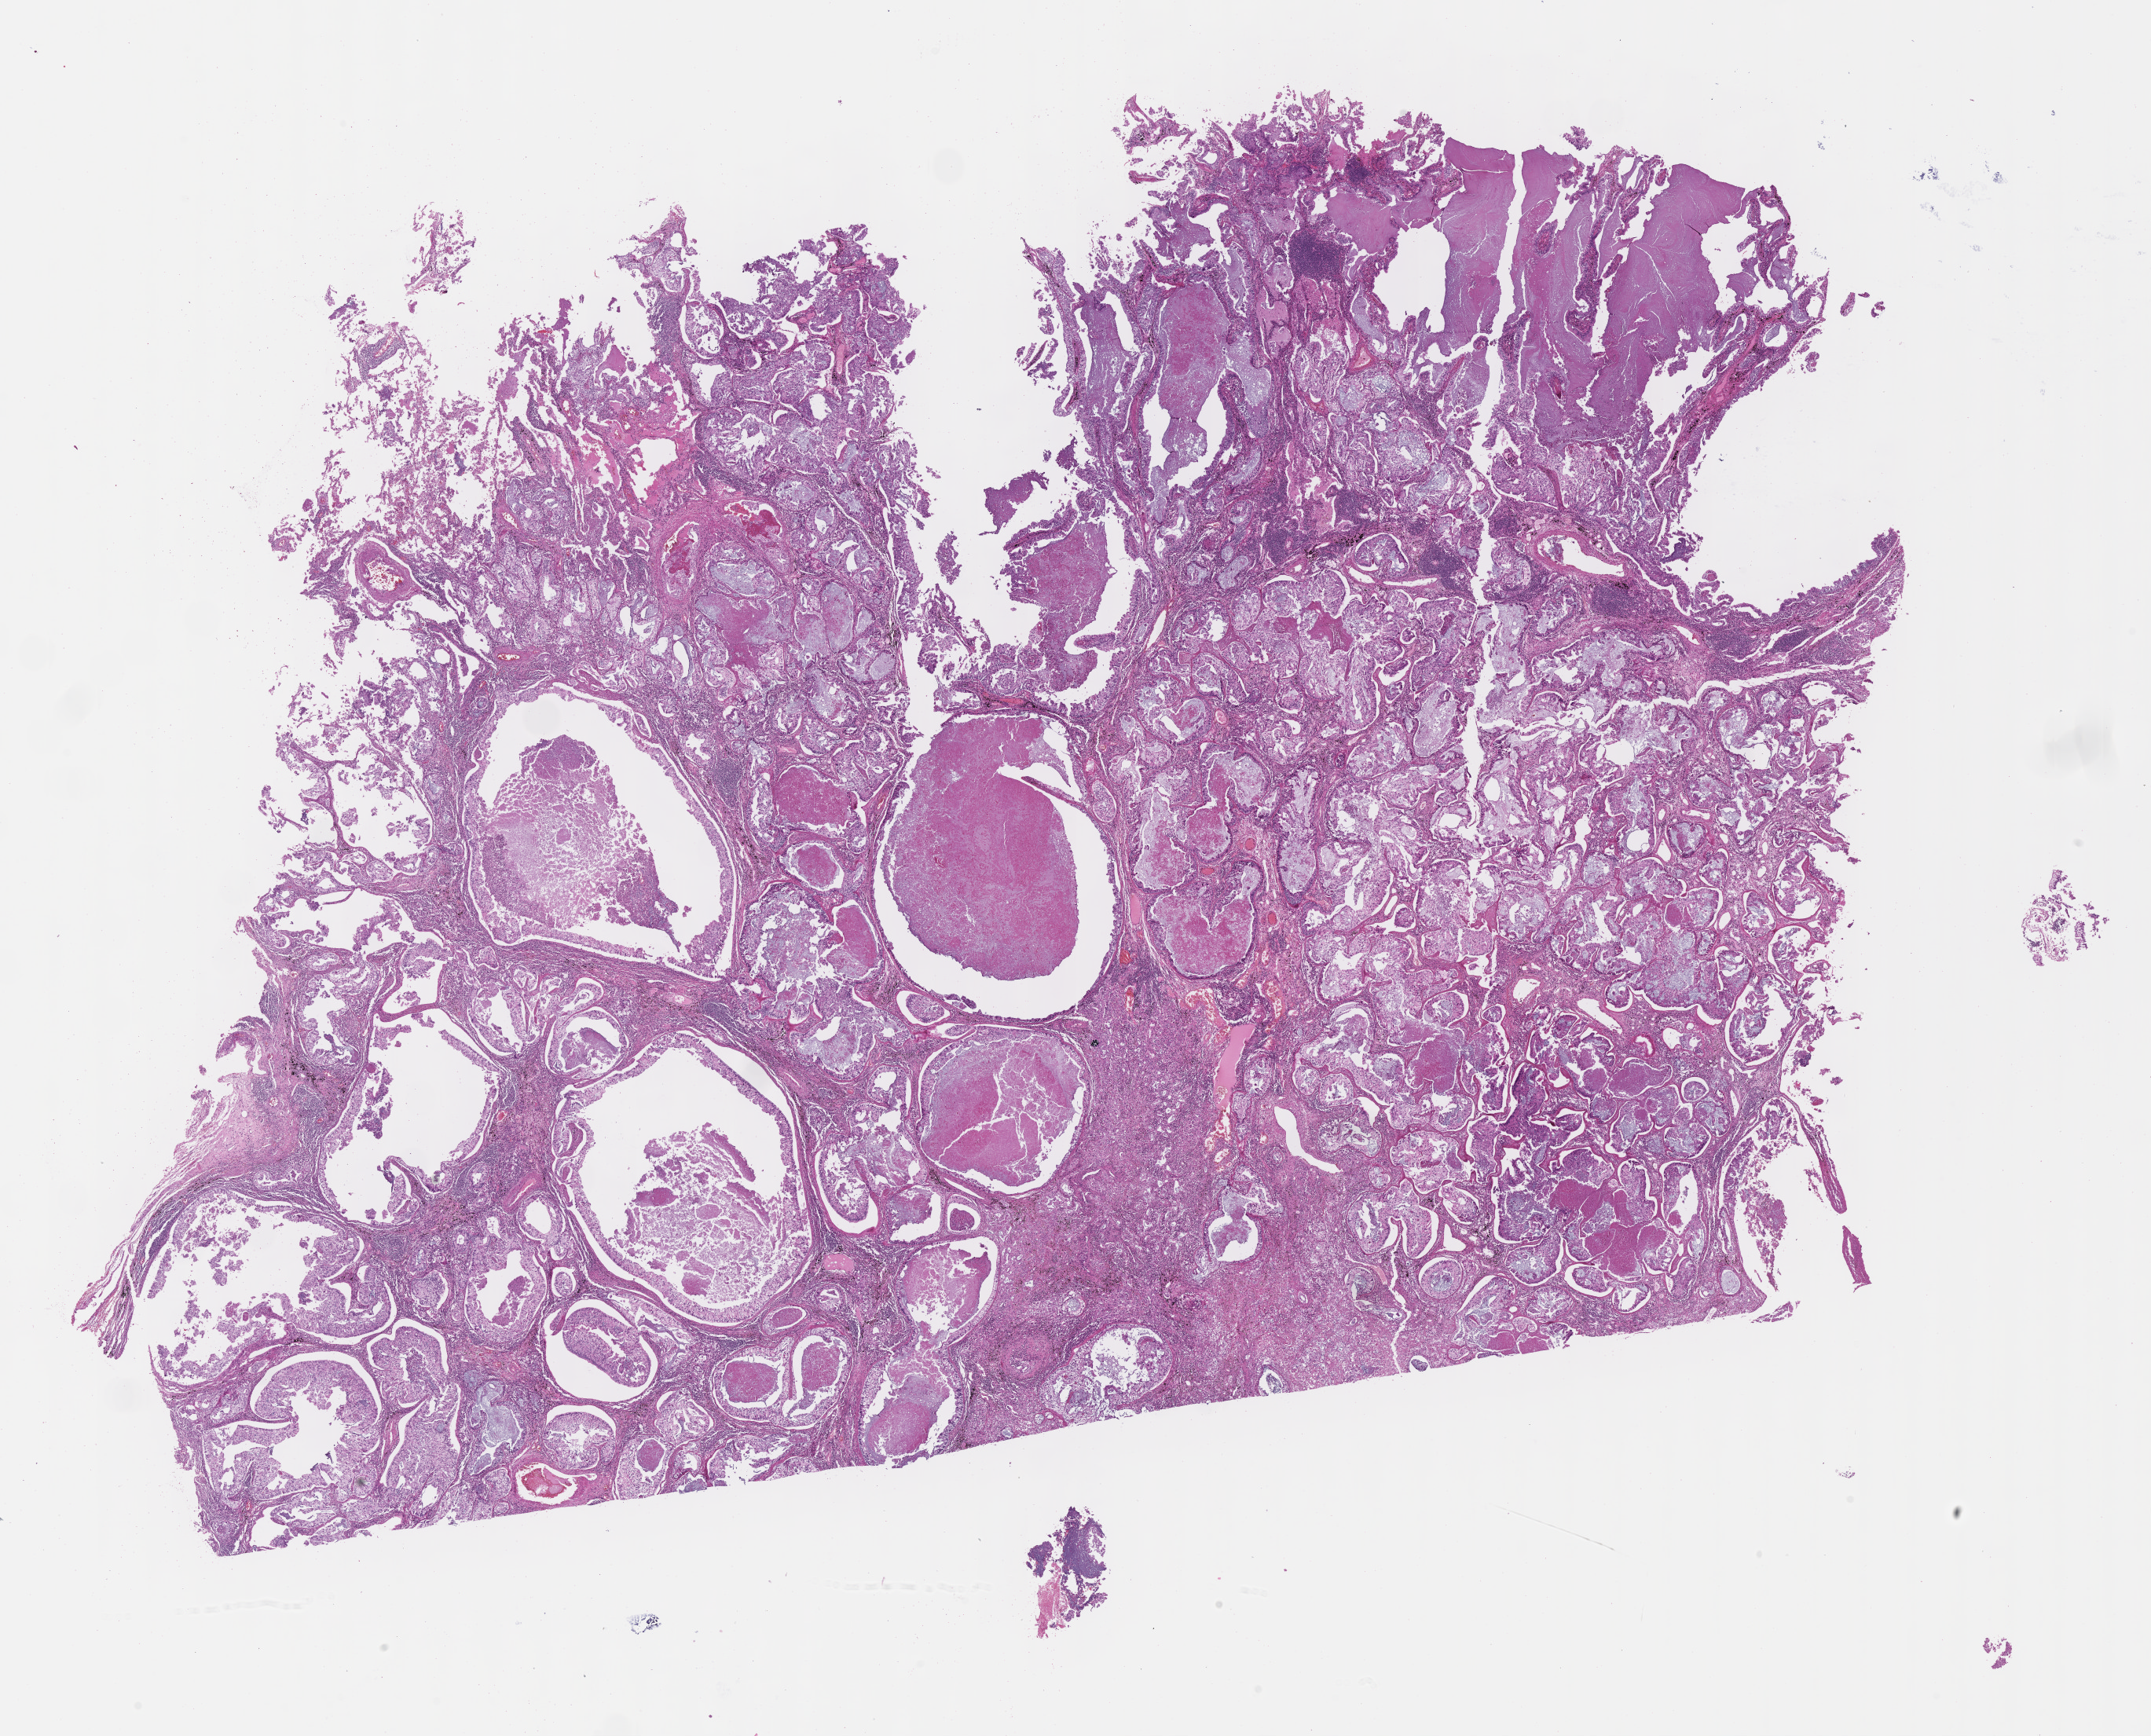
Whole-slide image, haematoxylin and eosin stain — low-resolution overview of the scanned area, about 22.1 x 17.9 mm; formalin-fixed, paraffin-embedded (FFPE) tissue; specimen: primary tumor; anatomic site: upper lobe of right lung. Patient female; 63 years old. Pathologist review of this section (percent, as recorded): tumor cells 60%, tumor nuclei 75%, stromal cells 15%, necrosis 15%, normal cells 10%. Infiltration values recorded for this section: lymphocyte infiltration 3%, monocyte infiltration 3%, neutrophil infiltration 1%.
Section: top of the tissue portion. AJCC pathologic stage: Stage IB. Histologic diagnosis: Adenocarcinoma, NOS.